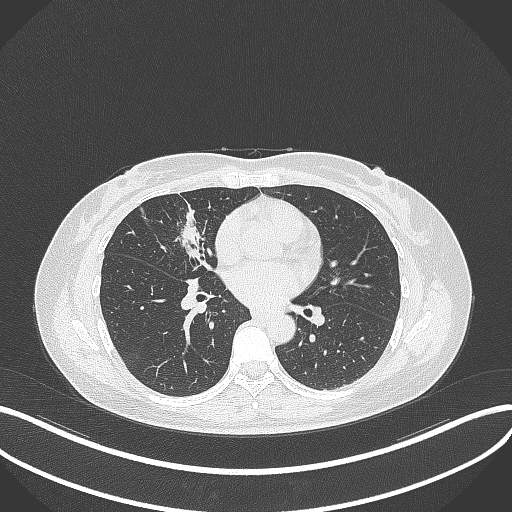
Chest CT, one axial slice. Position 142 of 284 along the scan axis. Reconstruction kernel B70f. 120 kVp. Lung window (W 1500 / L -600 HU). 1 mm slice thickness. 512 × 512 image matrix. Patient: female, 43 years. Case-level facts recorded for this patient, not image findings: clinical TNM (as recorded): T1c N3 M1.
Annotated regions visible in this slice (rectangle marked by the reading radiologist):
- lung tumour (recorded histology: adenocarcinoma): bounding box (x1, y1, x2, y2) in pixels: (173, 210, 210, 263)